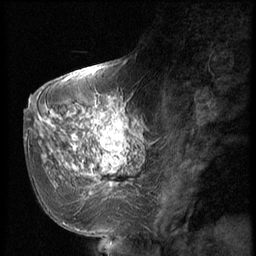
Breast MRI (dynamic contrast-enhanced), one sagittal slice; dynamic contrast-enhanced series, image 2 of 2 at this slice position (ordered by acquisition); 1.5 T; TE 4.2 ms, TR 9 ms; 2.5 mm slice thickness; 256 × 256 image matrix, field of view 180 × 180 mm. Female patient, age 51 years. From the clinical record (not read from this slice): setting: breast cancer imaged before/during neoadjuvant chemotherapy; receptor status: triple-negative.
Structures marked on this image (semi-automatically segmented with operator editing):
- analysis volume of interest (the breast-tissue region the enhancement analysis was run in; not a lesion): bounding box (x1, y1, x2, y2) in pixels: (60, 98, 147, 197)
- tumour enhancement mask (voxels above the 140 % enhancement threshold inside the analysis volume of interest): (66, 98, 135, 195)